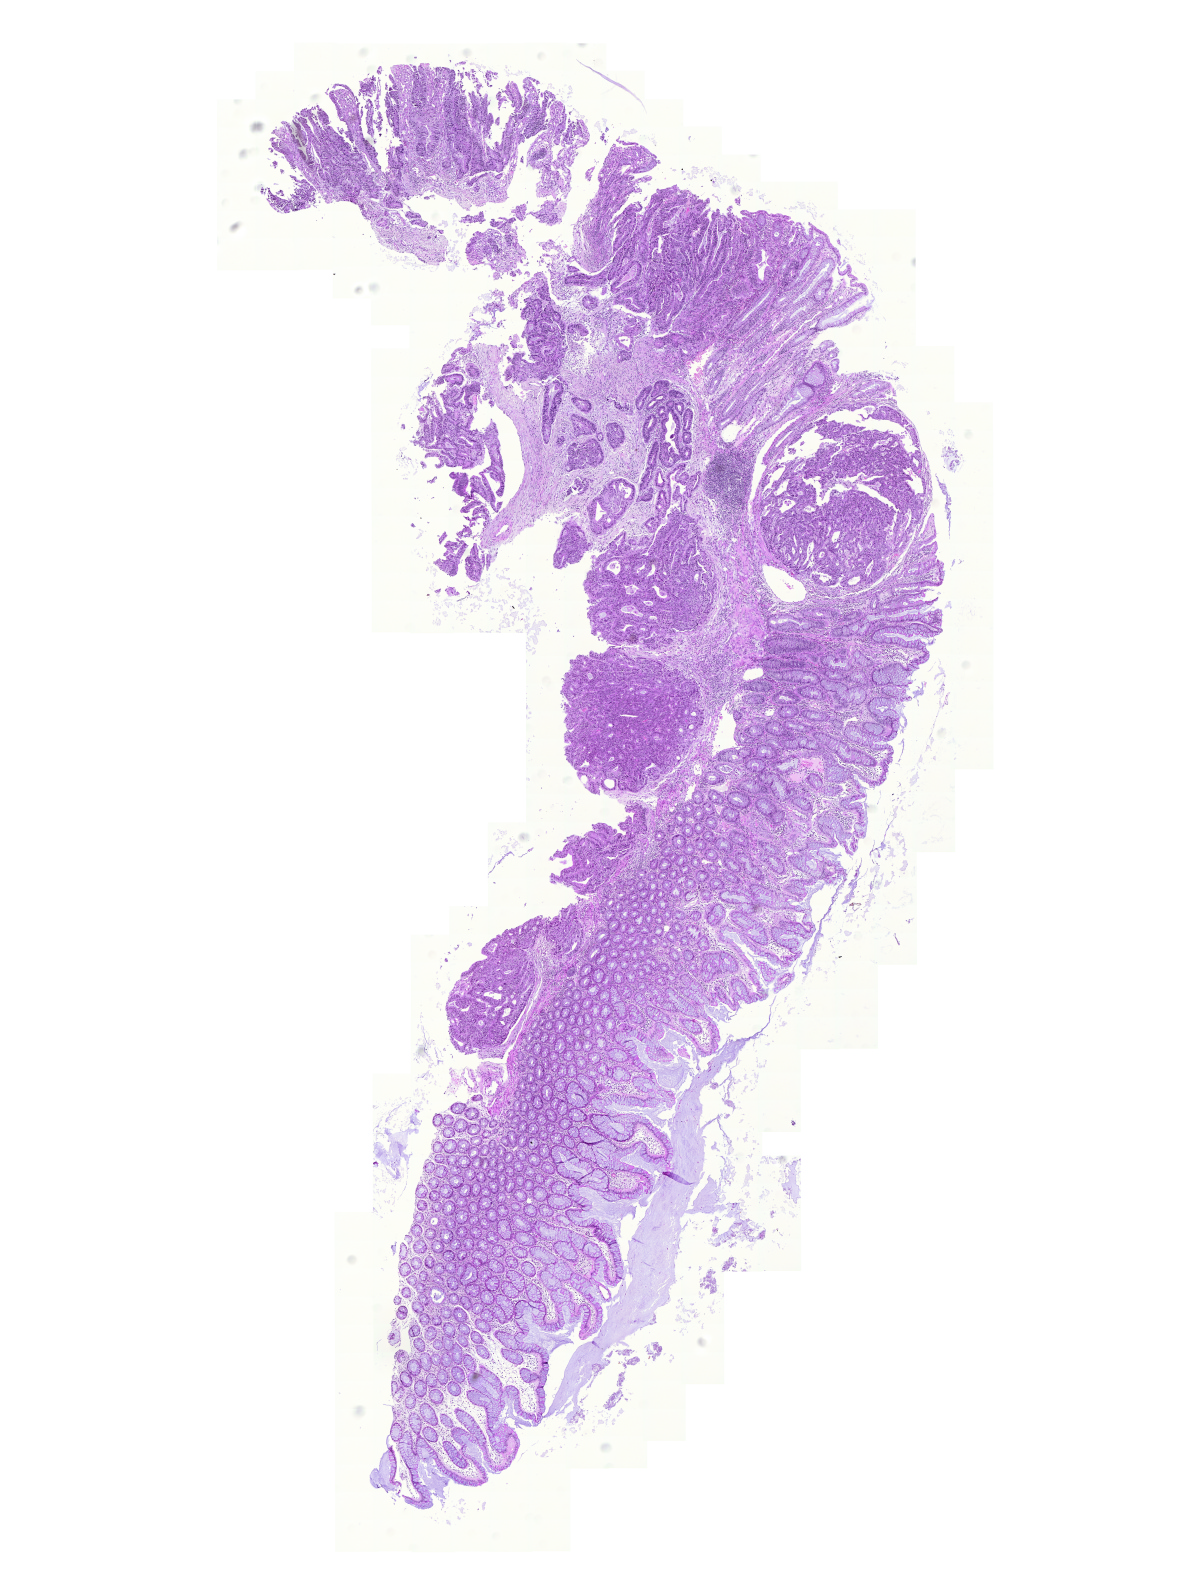
H&E whole-slide image, whole scanned area (about 8.9 x 11.7 mm, acquisition: 20x scan) shown as a low-resolution overview; formalin-fixed paraffin-embedded (FFPE) diagnostic section; rectum, primary tumour sample. Male, age 71 years at initial diagnosis.
- AJCC pathologic stage: III (5th edition)
- diagnosis: Adenocarcinoma, NOS
- TNM: T3 N2 M0